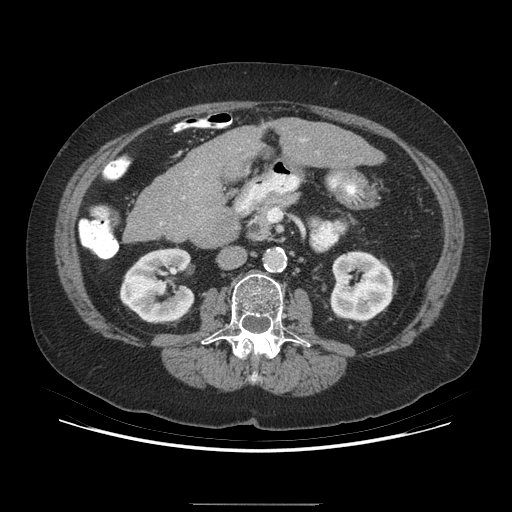
Contrast-enhanced abdominal CT (liver protocol), one axial slice. Reconstruction kernel STANDARD. 140 kVp. Soft-tissue window (W 400 / L 40 HU). 512 × 512 image matrix, field of view 400 × 400 mm. Case-level facts recorded for this patient, not image findings: diagnosis: hepatocellular carcinoma (patient treated with transarterial chemoembolisation; whether this scan precedes or follows treatment is not stated here); TNM stage (as recorded): Stage-I; Child-Pugh class: A; tumour nodularity: uninodular; tumour size: 3.2 cm.
Structures marked on this image (semi-automatically segmented with operator editing):
- liver parenchyma outside the tumour (the mass and vessels are separate outlines, so this box may not span the whole liver): box from (x=125, y=118) to (x=384, y=248) px
- mass: (x=225, y=151)–(x=255, y=182)